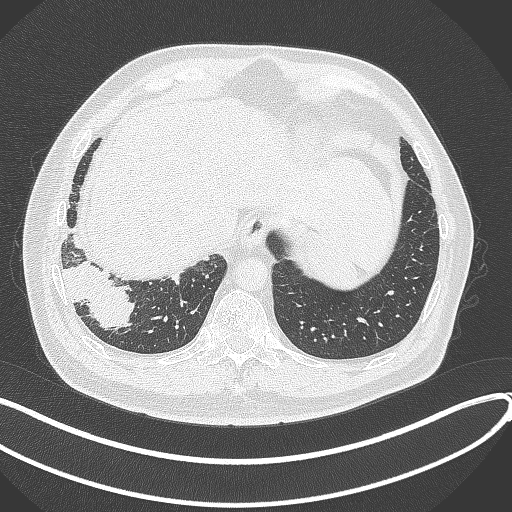
Chest CT, one axial slice; position 64 of 360 along the scan axis; reconstruction kernel B70f; lung window (W 1500 / L -600 HU); 512 × 512 image matrix. Patient: male, 59 years.
Annotated regions visible in this slice (bounding box drawn by a radiologist):
- lung tumour (recorded histology: adenocarcinoma): bounding box [x1, y1, x2, y2] px = [56, 252, 134, 334]